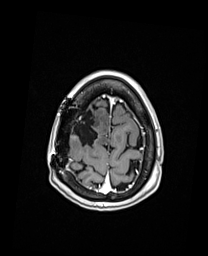
Brain MRI from a brain-tumour surgery series, one axial slice. Slice 34 of 192 in the series (ordered by position). T1-weighted post-contrast. 1 mm slice thickness. 208 × 256 image matrix, field of view 208 × 256 mm. Case-level facts recorded for this patient, not image findings: histopathology: Oligodendroglioma; WHO grade: 3; IDH mutation: yes; tumour location: Right Frontal.
Annotated regions visible in this slice (manually delineated by an expert):
- previous resection cavity: bounding box (x1, y1, x2, y2) in pixels: (72, 110, 99, 148)